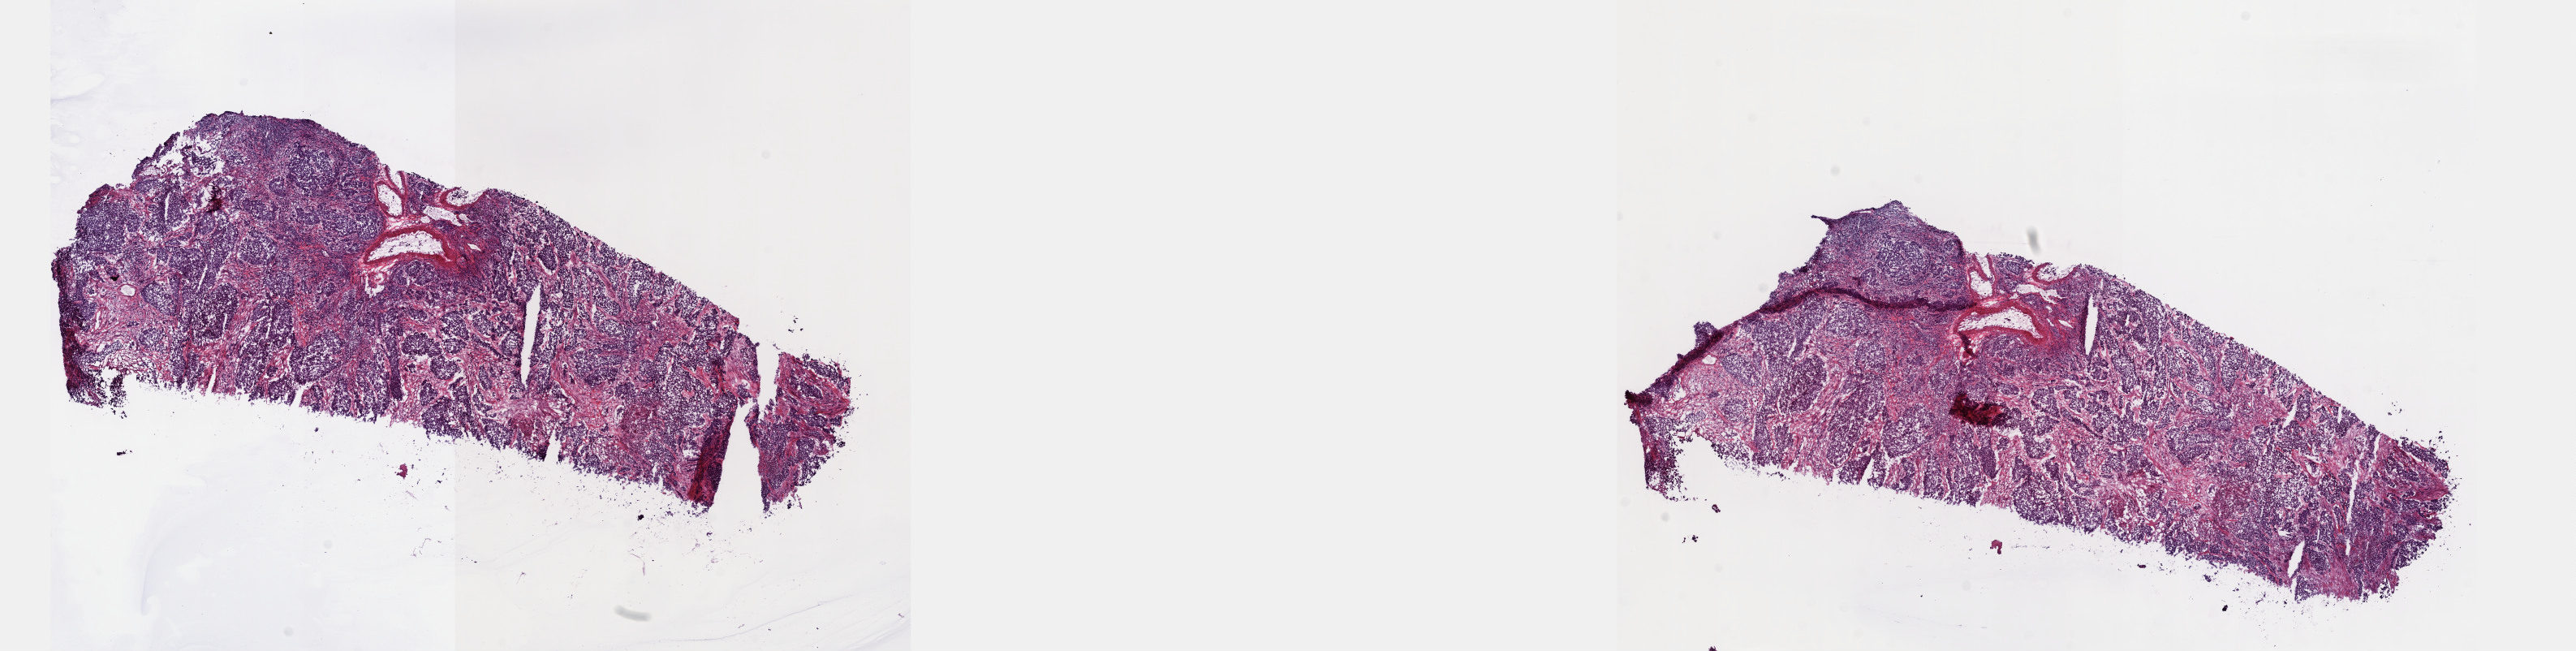
Whole-slide histology image, H&E, whole scanned area (about 25.7 x 6.5 mm, from a 40x scan) shown as a low-resolution overview. Frozen section from the top of the tissue portion. Sample: primary tumour, bladder. Male, age 68 years at initial diagnosis. Histologic grade: high grade. Composition of this section per pathologist review: tumour cells 70%, tumour nuclei 80%, normal cells 15%, stromal cells 15%, necrosis 0%. Inflammatory infiltration, as recorded: lymphocyte infiltration 0%, monocyte infiltration 0%, neutrophil infiltration 0%.
* pathologic diagnosis: Transitional cell carcinoma
* lymph nodes positive (case pathology): 0 of 79 examined
* TNM: T3b N0 MX
* AJCC pathologic stage: III